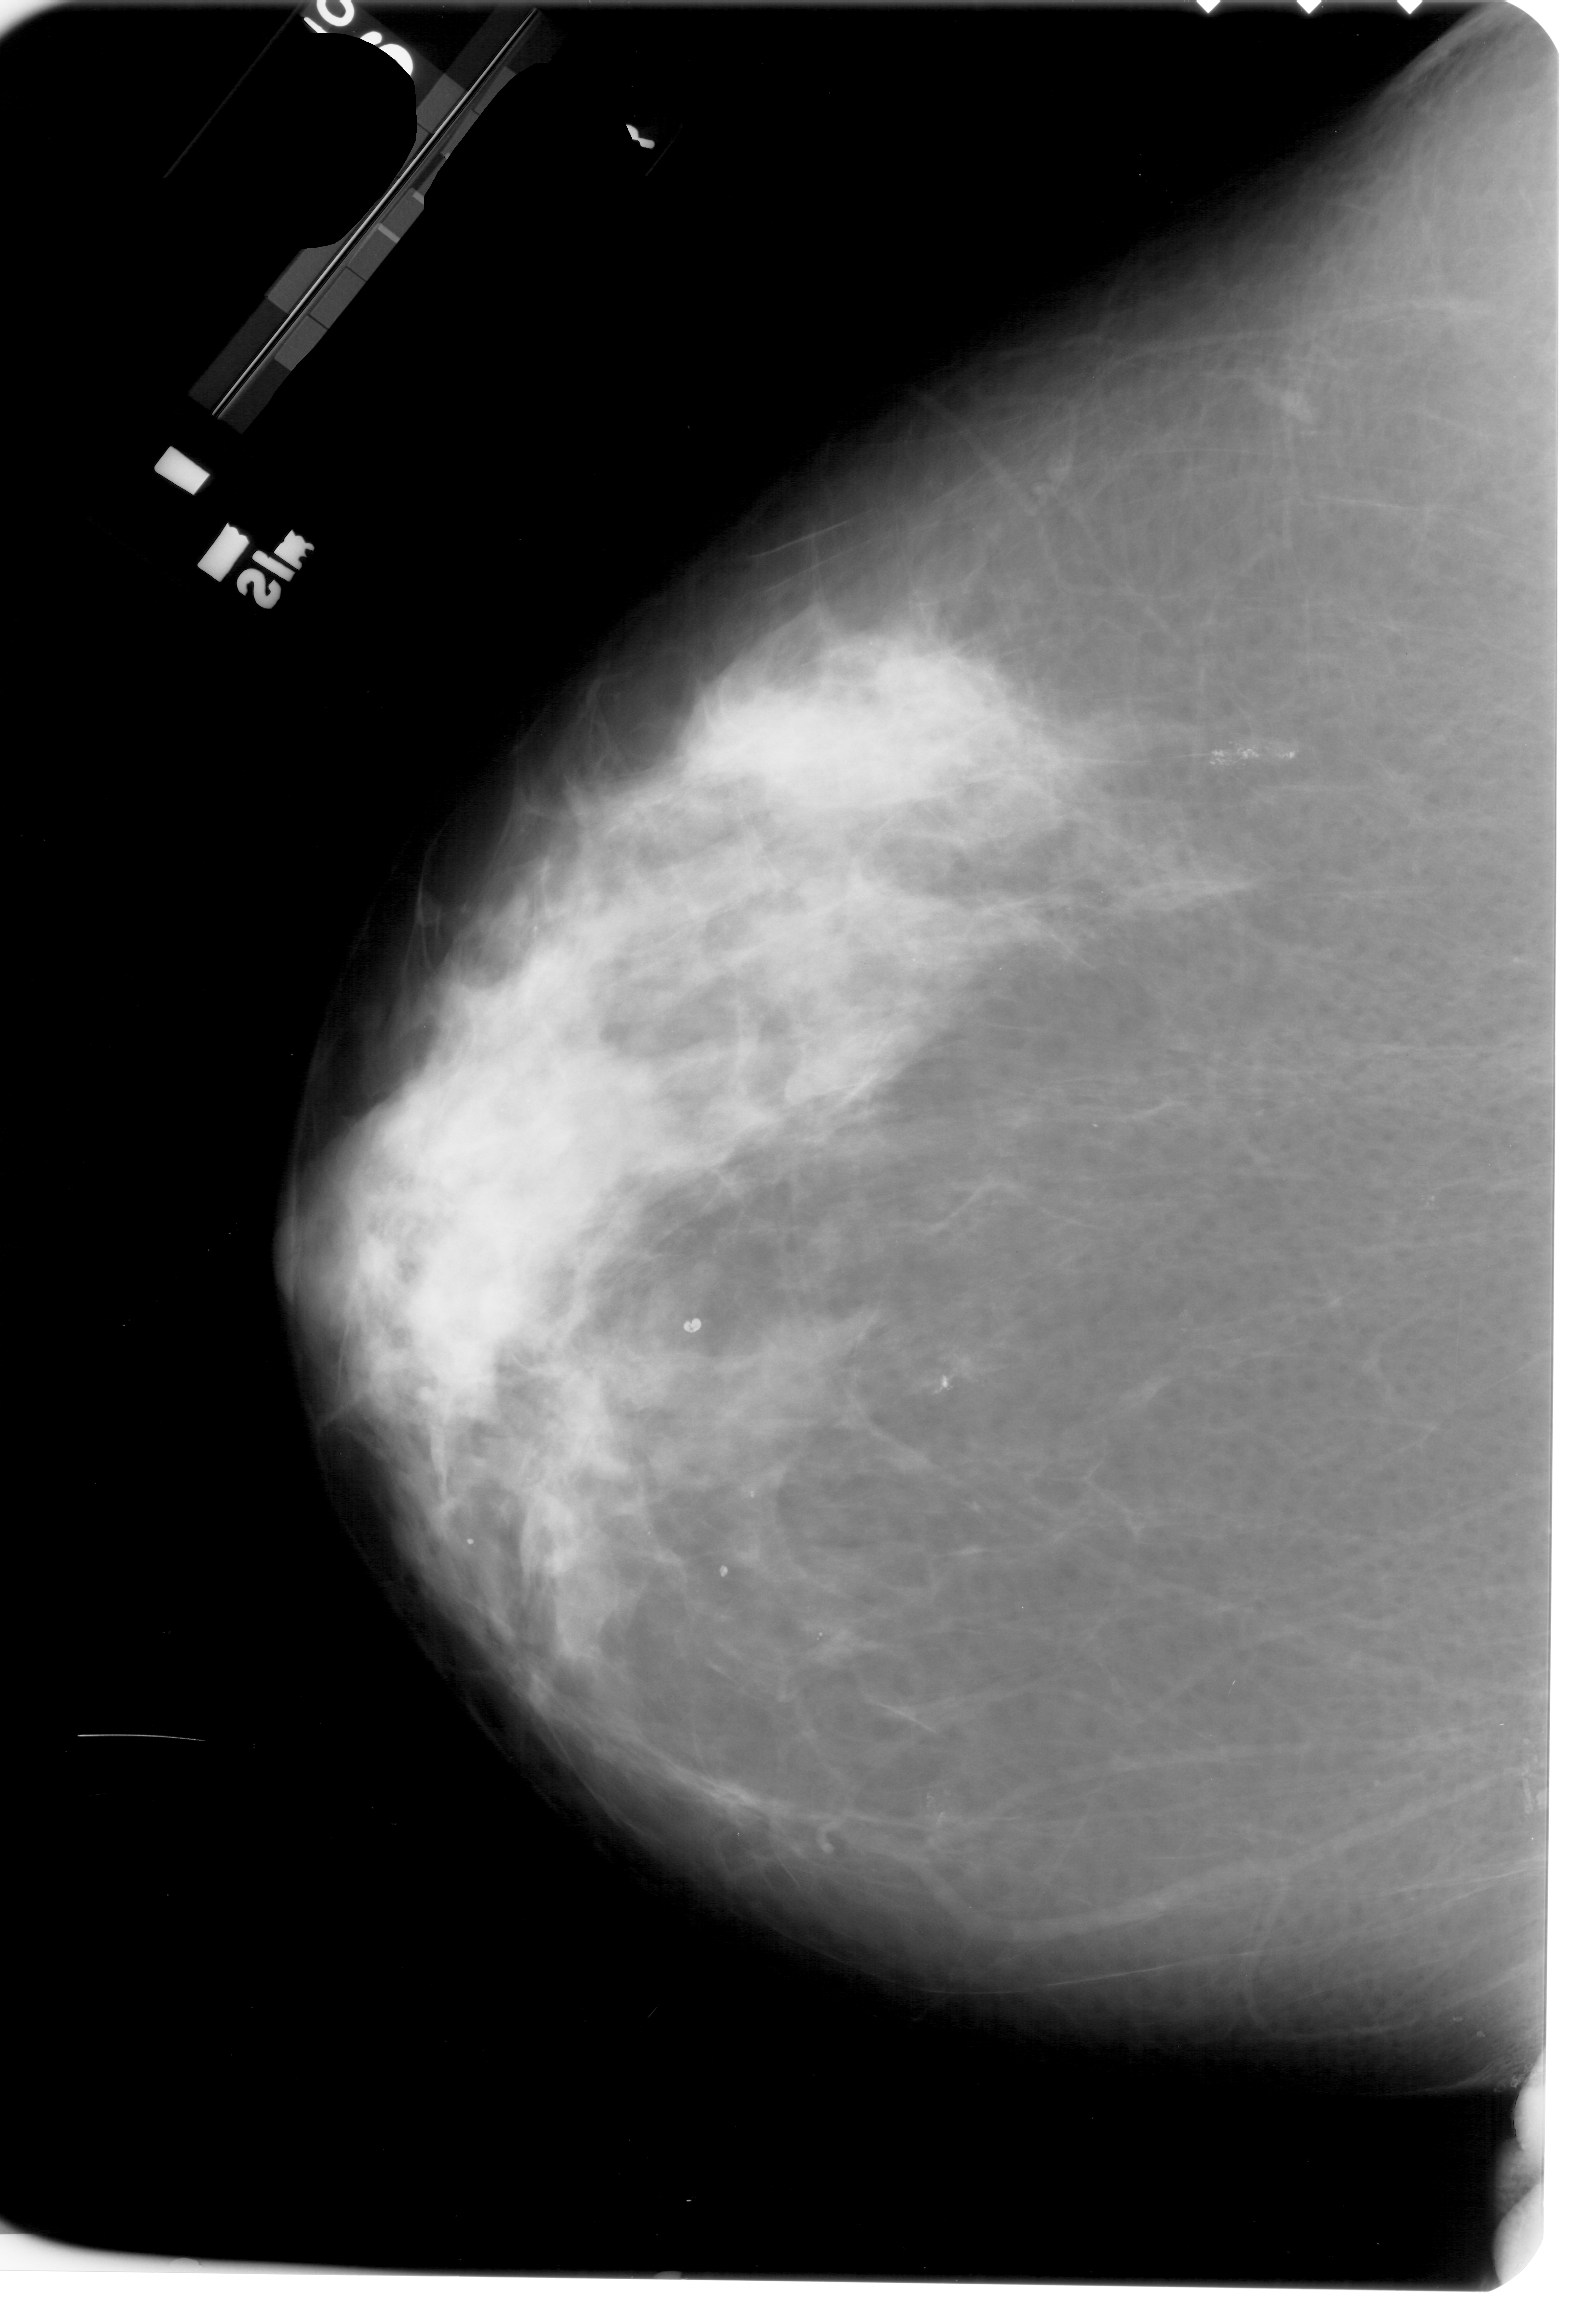
Digitized screen-film mammogram; left breast; CC view; 1573 × 2324 image matrix.
Marked abnormalities (boxes around the expert regions of interest):
- calcifications, morphology pleomorphic, distribution clustered; BI-RADS assessment category 4; pathology result (as recorded, not read from the image): benign: bounding box <907,1778,967,1841> (left, top, right, bottom; pixels)